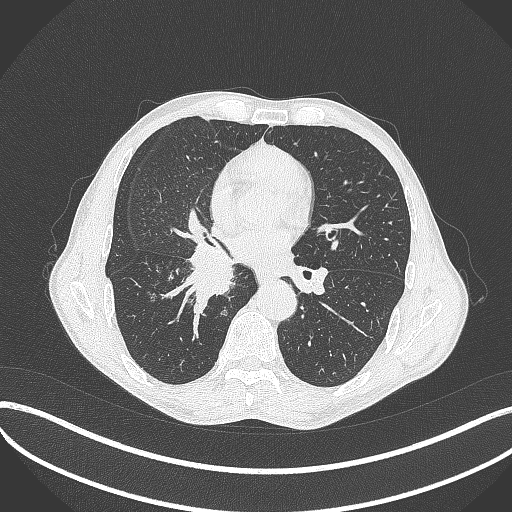
Chest CT, one axial slice; position 214 of 481 along the scan axis; reconstruction kernel B70f; 120 kVp; lung window (W 1500 / L -600 HU); 1 mm slice thickness; 512 × 512 image matrix, field of view 400 × 400 mm. Patient: male, 65 years. From the clinical record (not read from this slice): clinical TNM (as recorded): T2a N0 M0; histopathological grade: G2.
Structures marked on this image (rectangle marked by the reading radiologist):
- lung tumour (recorded histology: squamous cell carcinoma): bounding box [x1, y1, x2, y2] px = [180, 240, 244, 314]